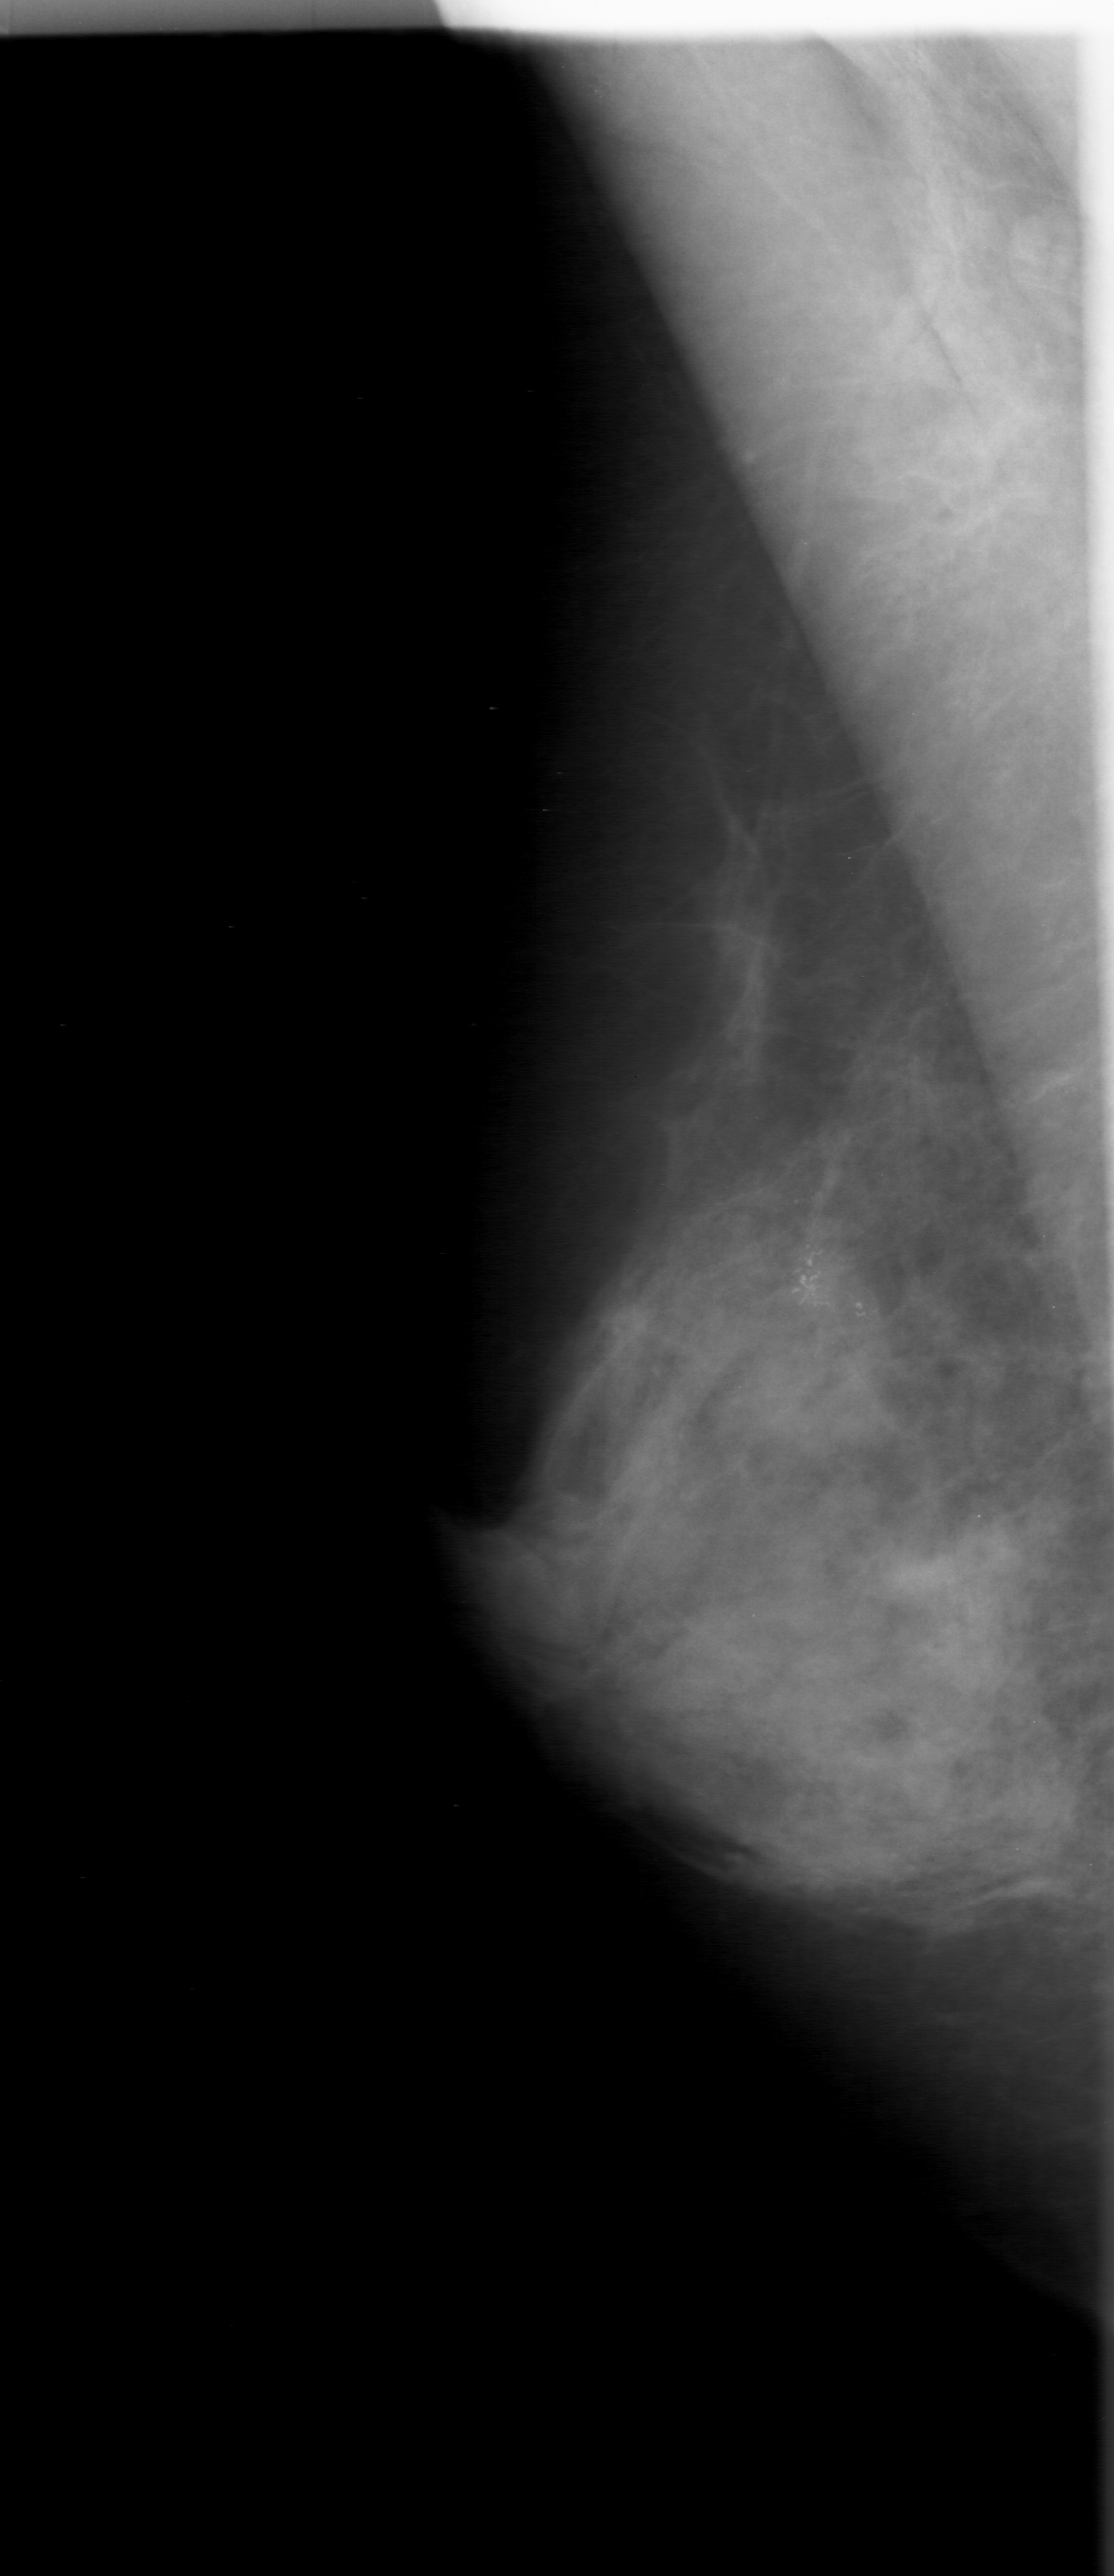
Scanned film-screen mammogram, right breast, mediolateral oblique (MLO) view, BI-RADS breast density category 3 (scale 1–4).
- Radiologist-marked abnormalities on this image: calcifications, morphology fine linear branching, distribution clustered; BI-RADS assessment category 3; subtlety rating 5 on a 1 (subtle) to 5 (obvious) scale; pathology result (as recorded, not read from the image): malignant.